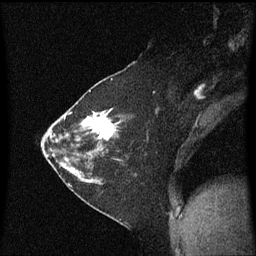
Breast MRI (dynamic contrast-enhanced), one sagittal slice; slice 34 of 60 in the series (ordered by position); dynamic contrast-enhanced series, image 2 of 3 at this slice position (ordered by acquisition); 1.5 T; TE 4.2 ms, TR 8.4 ms; 2 mm slice thickness; 256 × 256 image matrix, field of view 200 × 200 mm. Female patient, age 36 years. From the clinical record (not read from this slice): setting: breast cancer imaged before/during neoadjuvant chemotherapy; receptor status: HR-positive, HER2-negative.
Outlined on this slice (semi-automatic segmentation, software-assisted and operator-edited):
- analysis volume of interest (the breast-tissue region the enhancement analysis was run in; not a lesion): box from (x=66, y=102) to (x=120, y=179) px
- tumour enhancement mask (voxels above the 70 % enhancement threshold inside the analysis volume of interest): (x=82, y=110)–(x=117, y=141)